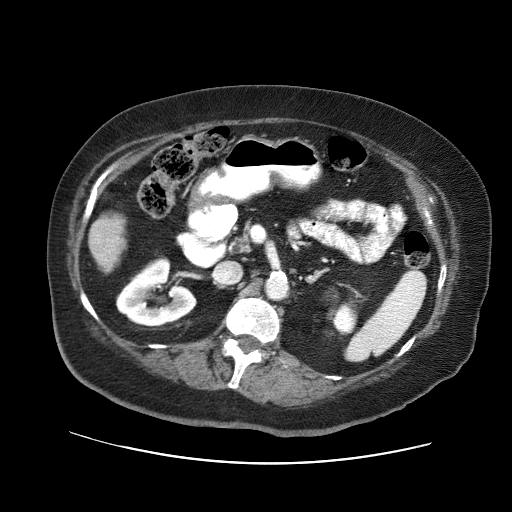
Contrast-enhanced abdominal CT (liver protocol), one axial slice; position 12 of 71 along the scan axis; reconstruction kernel STANDARD; 120 kVp; soft-tissue window (W 400 / L 40 HU); 2.5 mm slice thickness; 512 × 512 image matrix, field of view 400 × 400 mm. From the clinical record (not read from this slice): diagnosis: hepatocellular carcinoma (patient treated with transarterial chemoembolisation; whether this scan precedes or follows treatment is not stated here); TNM stage (as recorded): Stage-II; Child-Pugh class: A; tumour differentiation: poorly differentiated.
Outlined on this slice (semi-automatically segmented with operator editing):
- liver parenchyma outside the tumour (the mass and vessels are separate outlines, so this box may not span the whole liver): bounding box <88,212,126,272> (left, top, right, bottom; pixels)